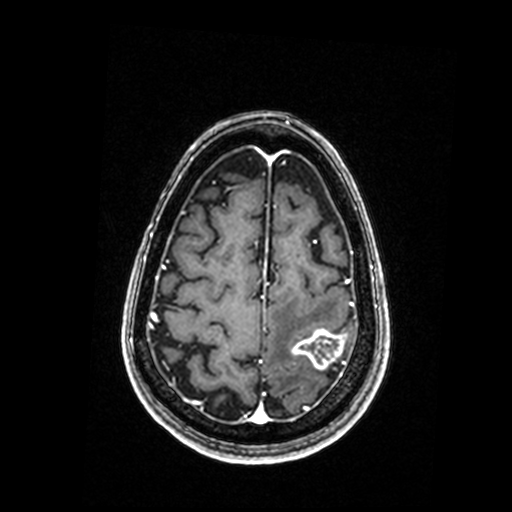
Brain MRI from a brain-tumour surgery series, one axial slice. Slice 50 of 192 in the series (ordered by position). T1-weighted post-contrast. 512 × 512 image matrix, field of view 250 × 250 mm. Case-level facts recorded for this patient, not image findings: histopathology: Metastastic Carcinoma, Poorly Differentiated; tumour location: Left Parietal.
Structures marked on this image (outlined manually by an expert reader):
- tumour: bounding box <292,330,345,369> (left, top, right, bottom; pixels)